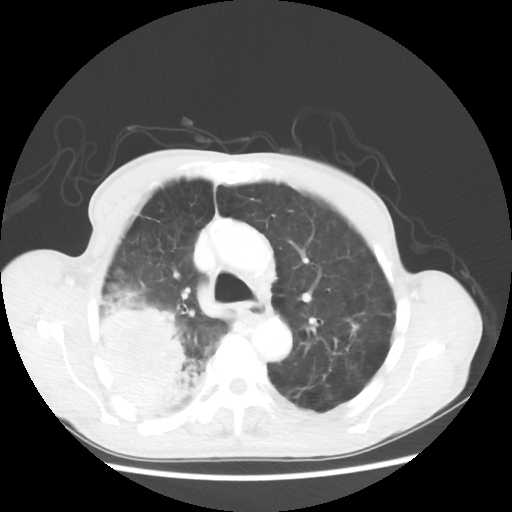
Chest CT, one axial slice; slice 39 of 58 in the series (ordered by position); reconstruction kernel STANDARD; 100 kVp; lung window (W 1500 / L -600 HU); 512 × 512 image matrix, field of view 351 × 351 mm. Male patient, age 75 years. From the clinical record (not read from this slice): clinical TNM (as recorded): T4 N1 M1.
Outlined on this slice (bounding box drawn by a radiologist):
- lung tumour (recorded histology: adenocarcinoma): bounding box (x1, y1, x2, y2) in pixels: (93, 281, 210, 420)